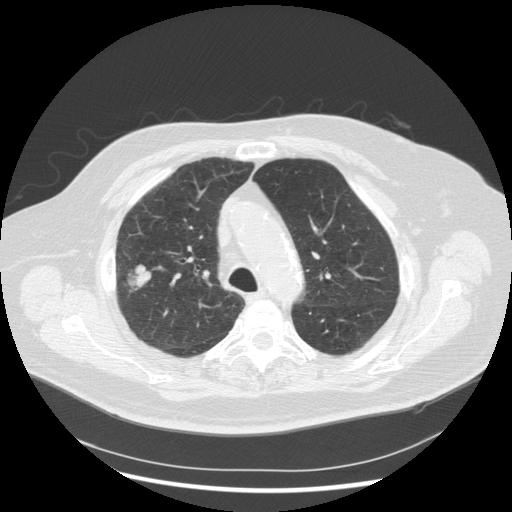
Low-dose screening chest CT, axial slice; third annual screen; lung window (W 1500 / L -600 HU); 120 kVp; slice 205 of 263 in the series; 512 × 512 image matrix. Male, age 72 years at enrolment. Former smoker at enrolment.
Expert-annotated lung lesion, bounding box (x1, y1, x2, y2) in pixels: (111, 252, 164, 302). Reader record for this screening exam (exam-level; its link to the box is not recorded): non-calcified nodule or mass ≥4 mm, right upper lobe, 31 × 31 mm, poorly defined margins, soft tissue attenuation, pre-existing on the prior screen: no. Official screen result: positive, other. Lung cancer was diagnosed 70 days after this screen: squamous cell carcinoma, NOS, right upper lobe, poorly differentiated (G3), stage IIIA (AJCC 6th edition), 19 mm at pathology.